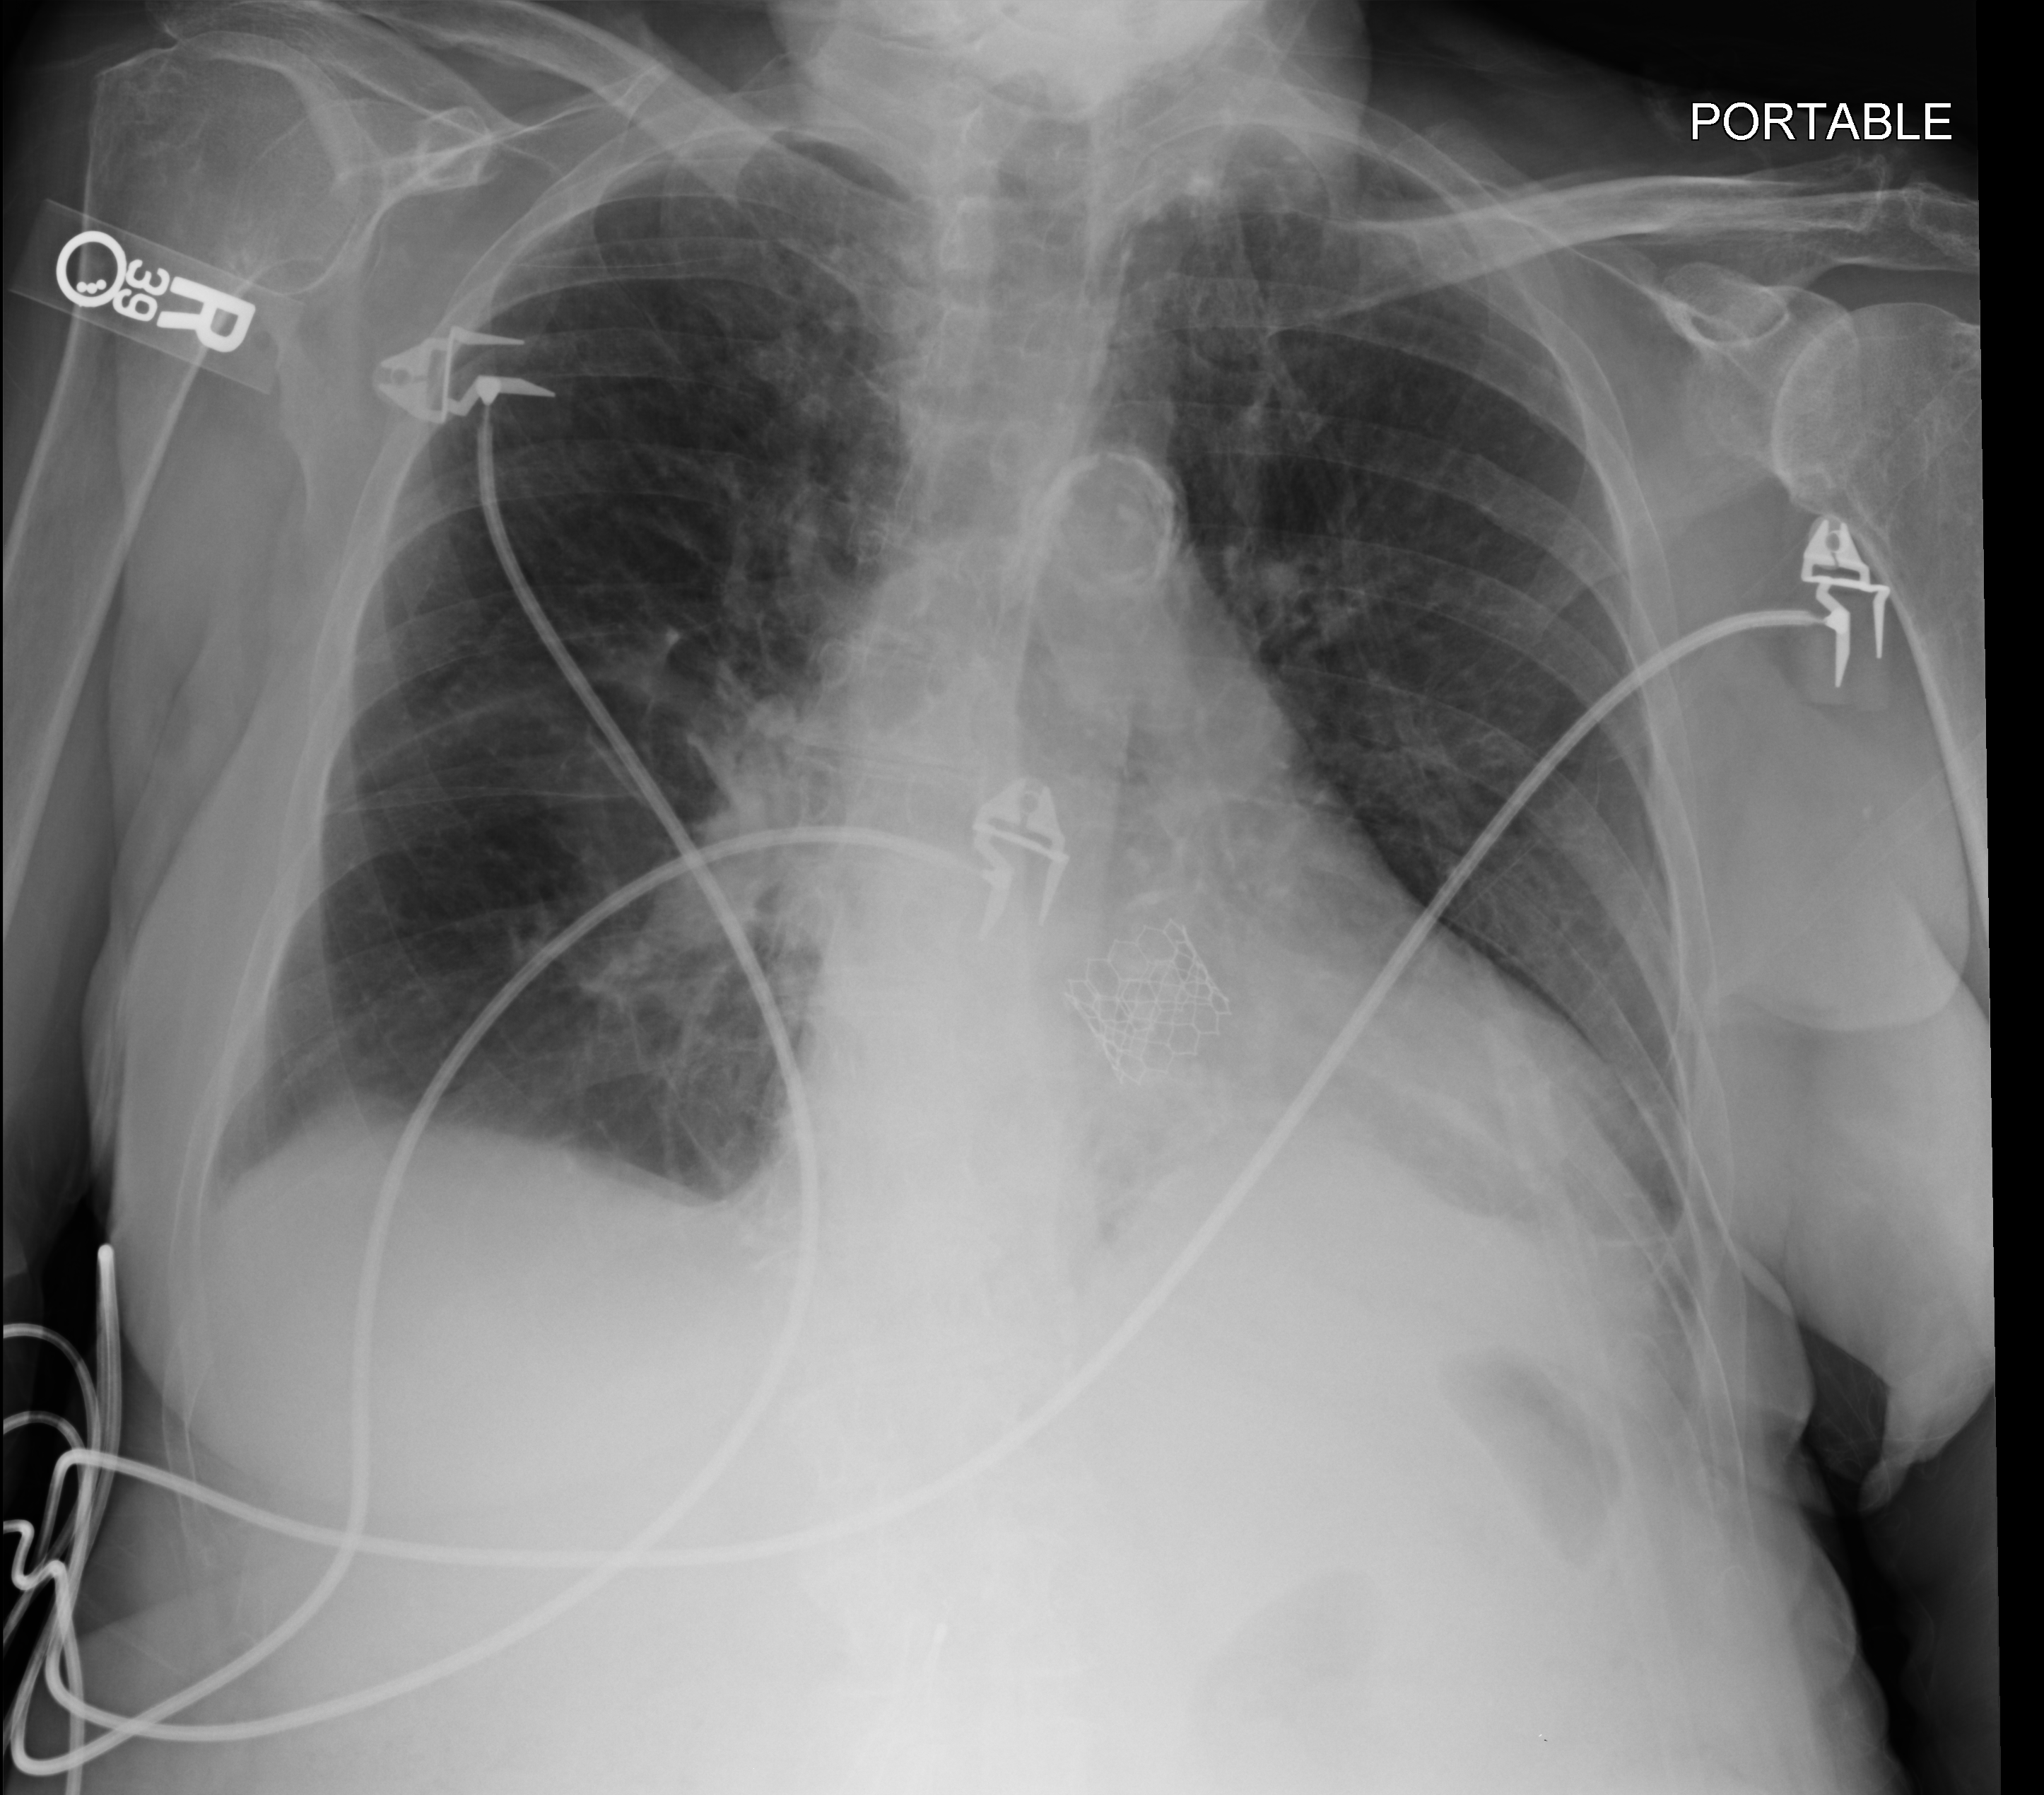
Bedside chest radiograph (computed radiography). Female patient hospitalised with COVID-19, age 75–90 years.
Admission-level facts for this patient (not findings on this image; timing relative to this image not recorded):
- length of hospital stay: 5 days
- smoking status (admission record): former